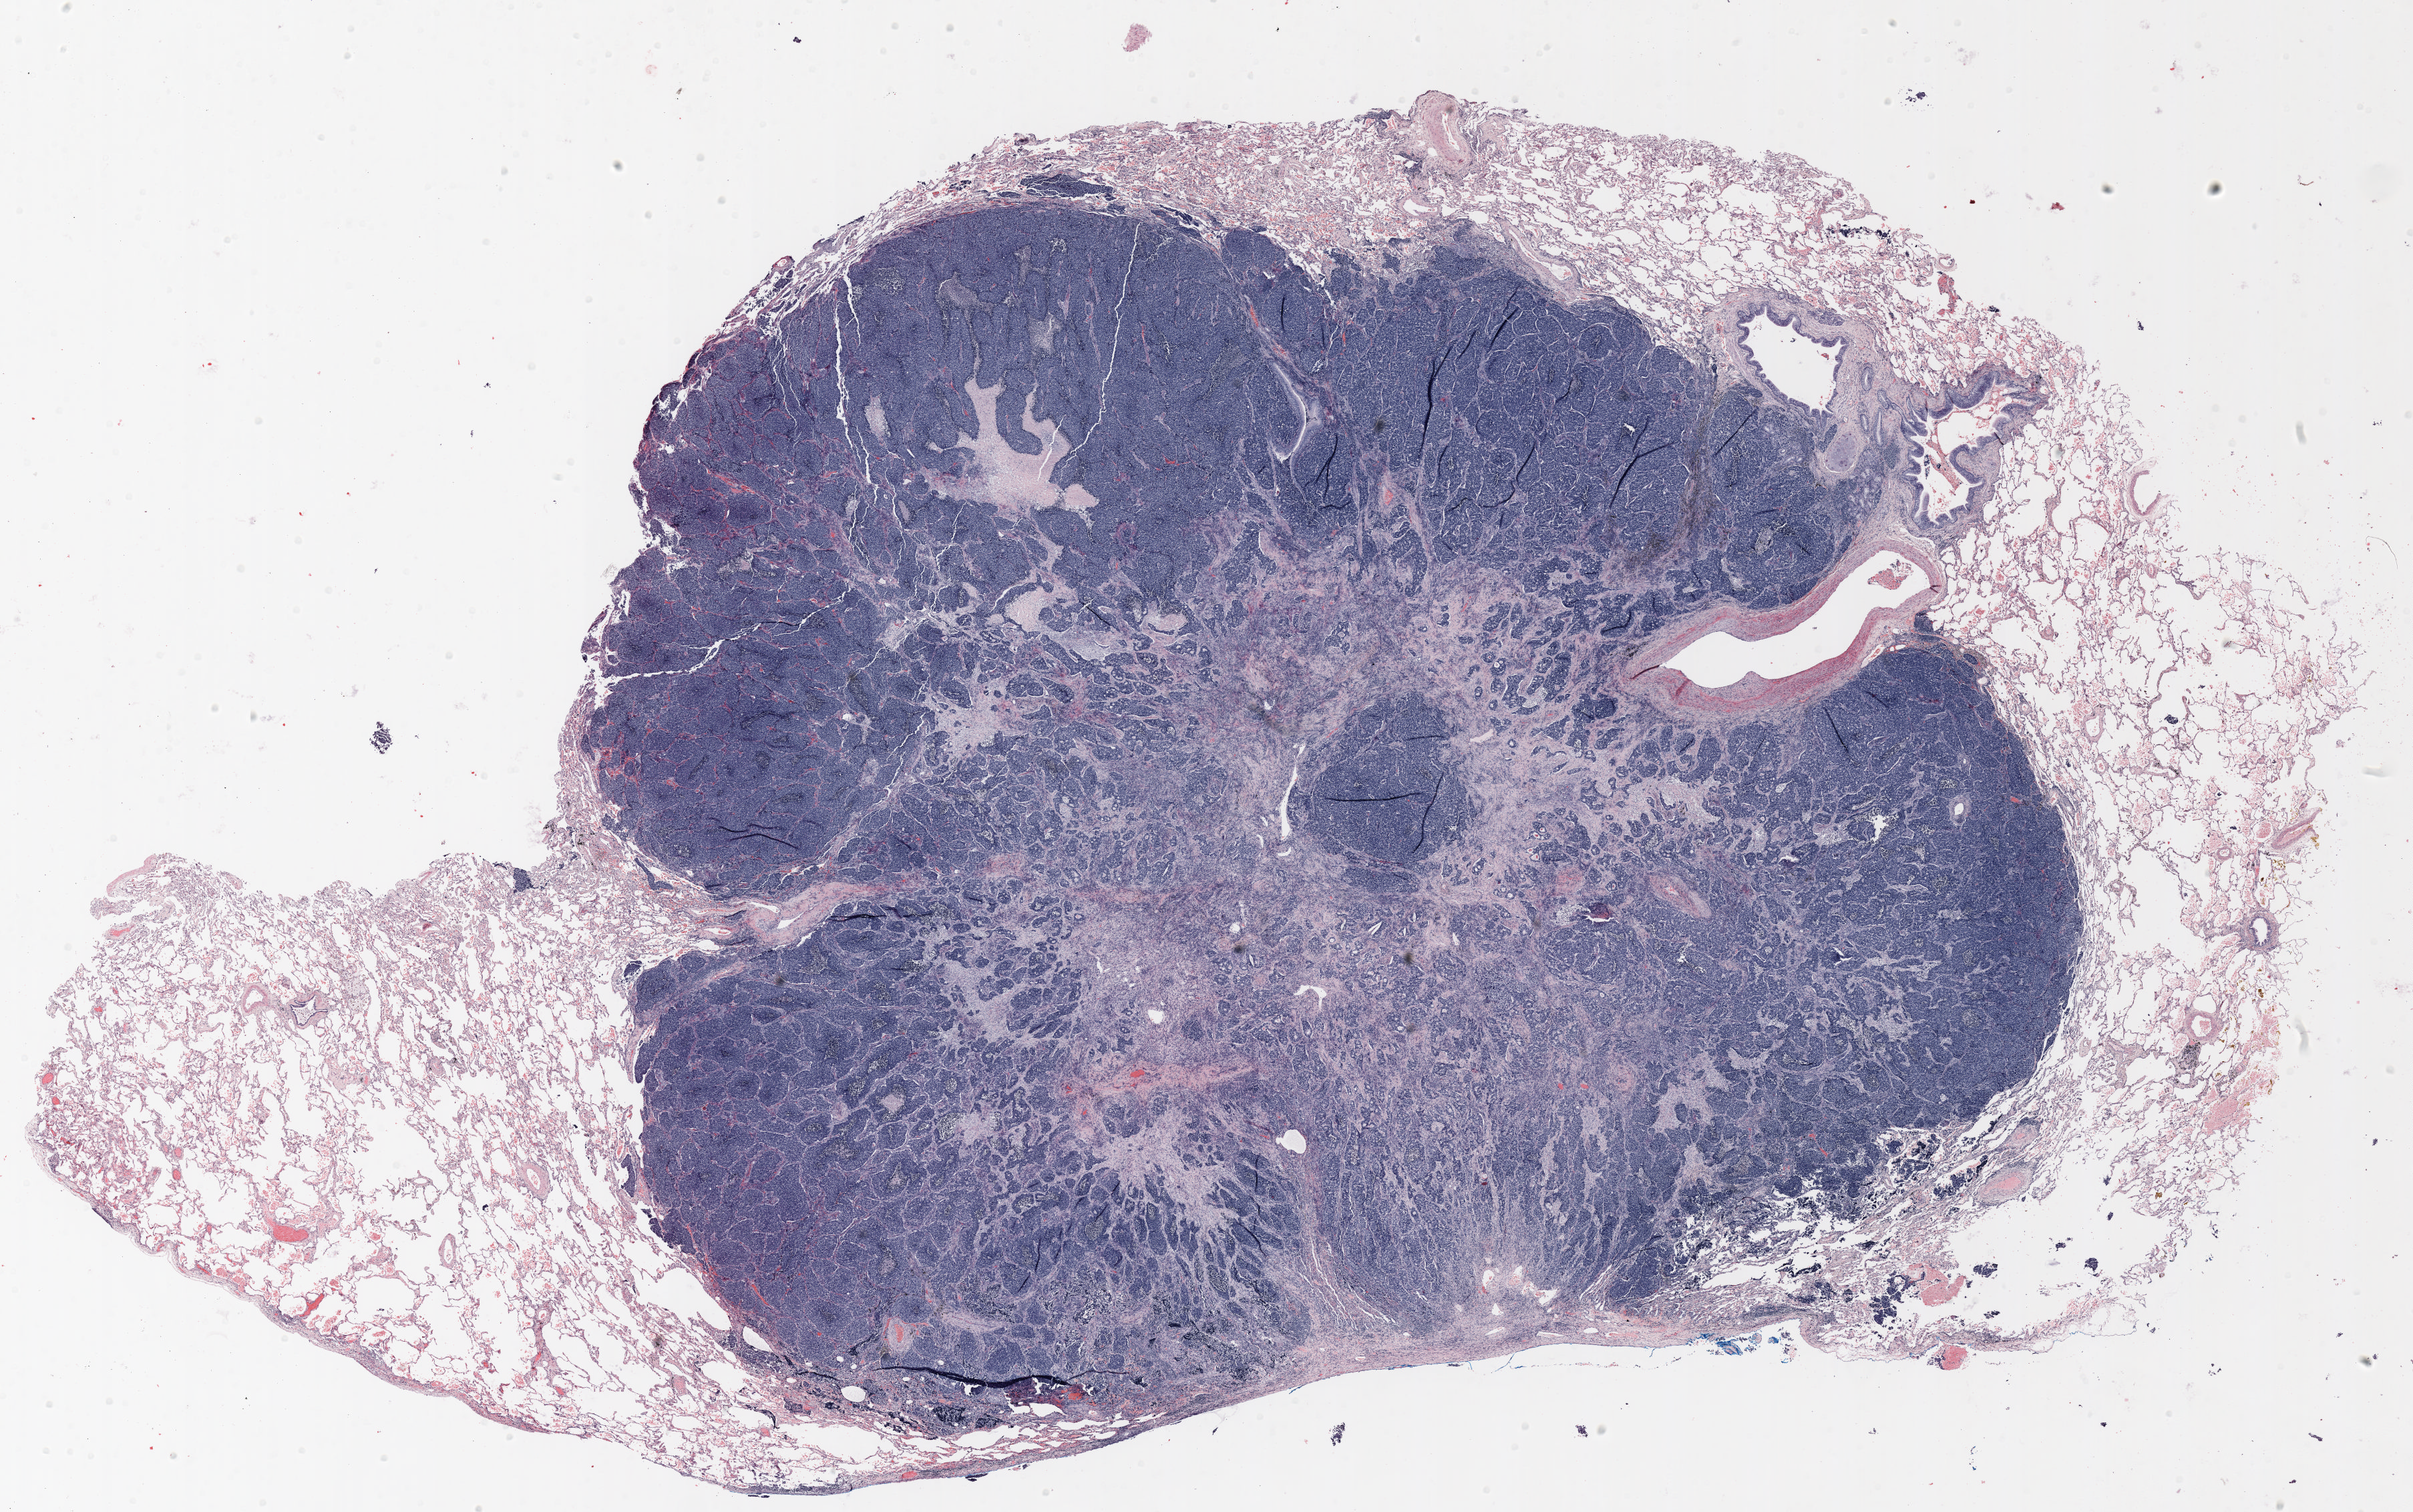
H&E whole-slide image, low-resolution overview of the scanned area, about 29.0 x 18.2 mm (slide scanned at 20x). Formalin-fixed paraffin-embedded (FFPE) section. Lung. Female, age 61 at enrolment.
Participant's lung-cancer diagnosis: Non-small cell carcinoma.